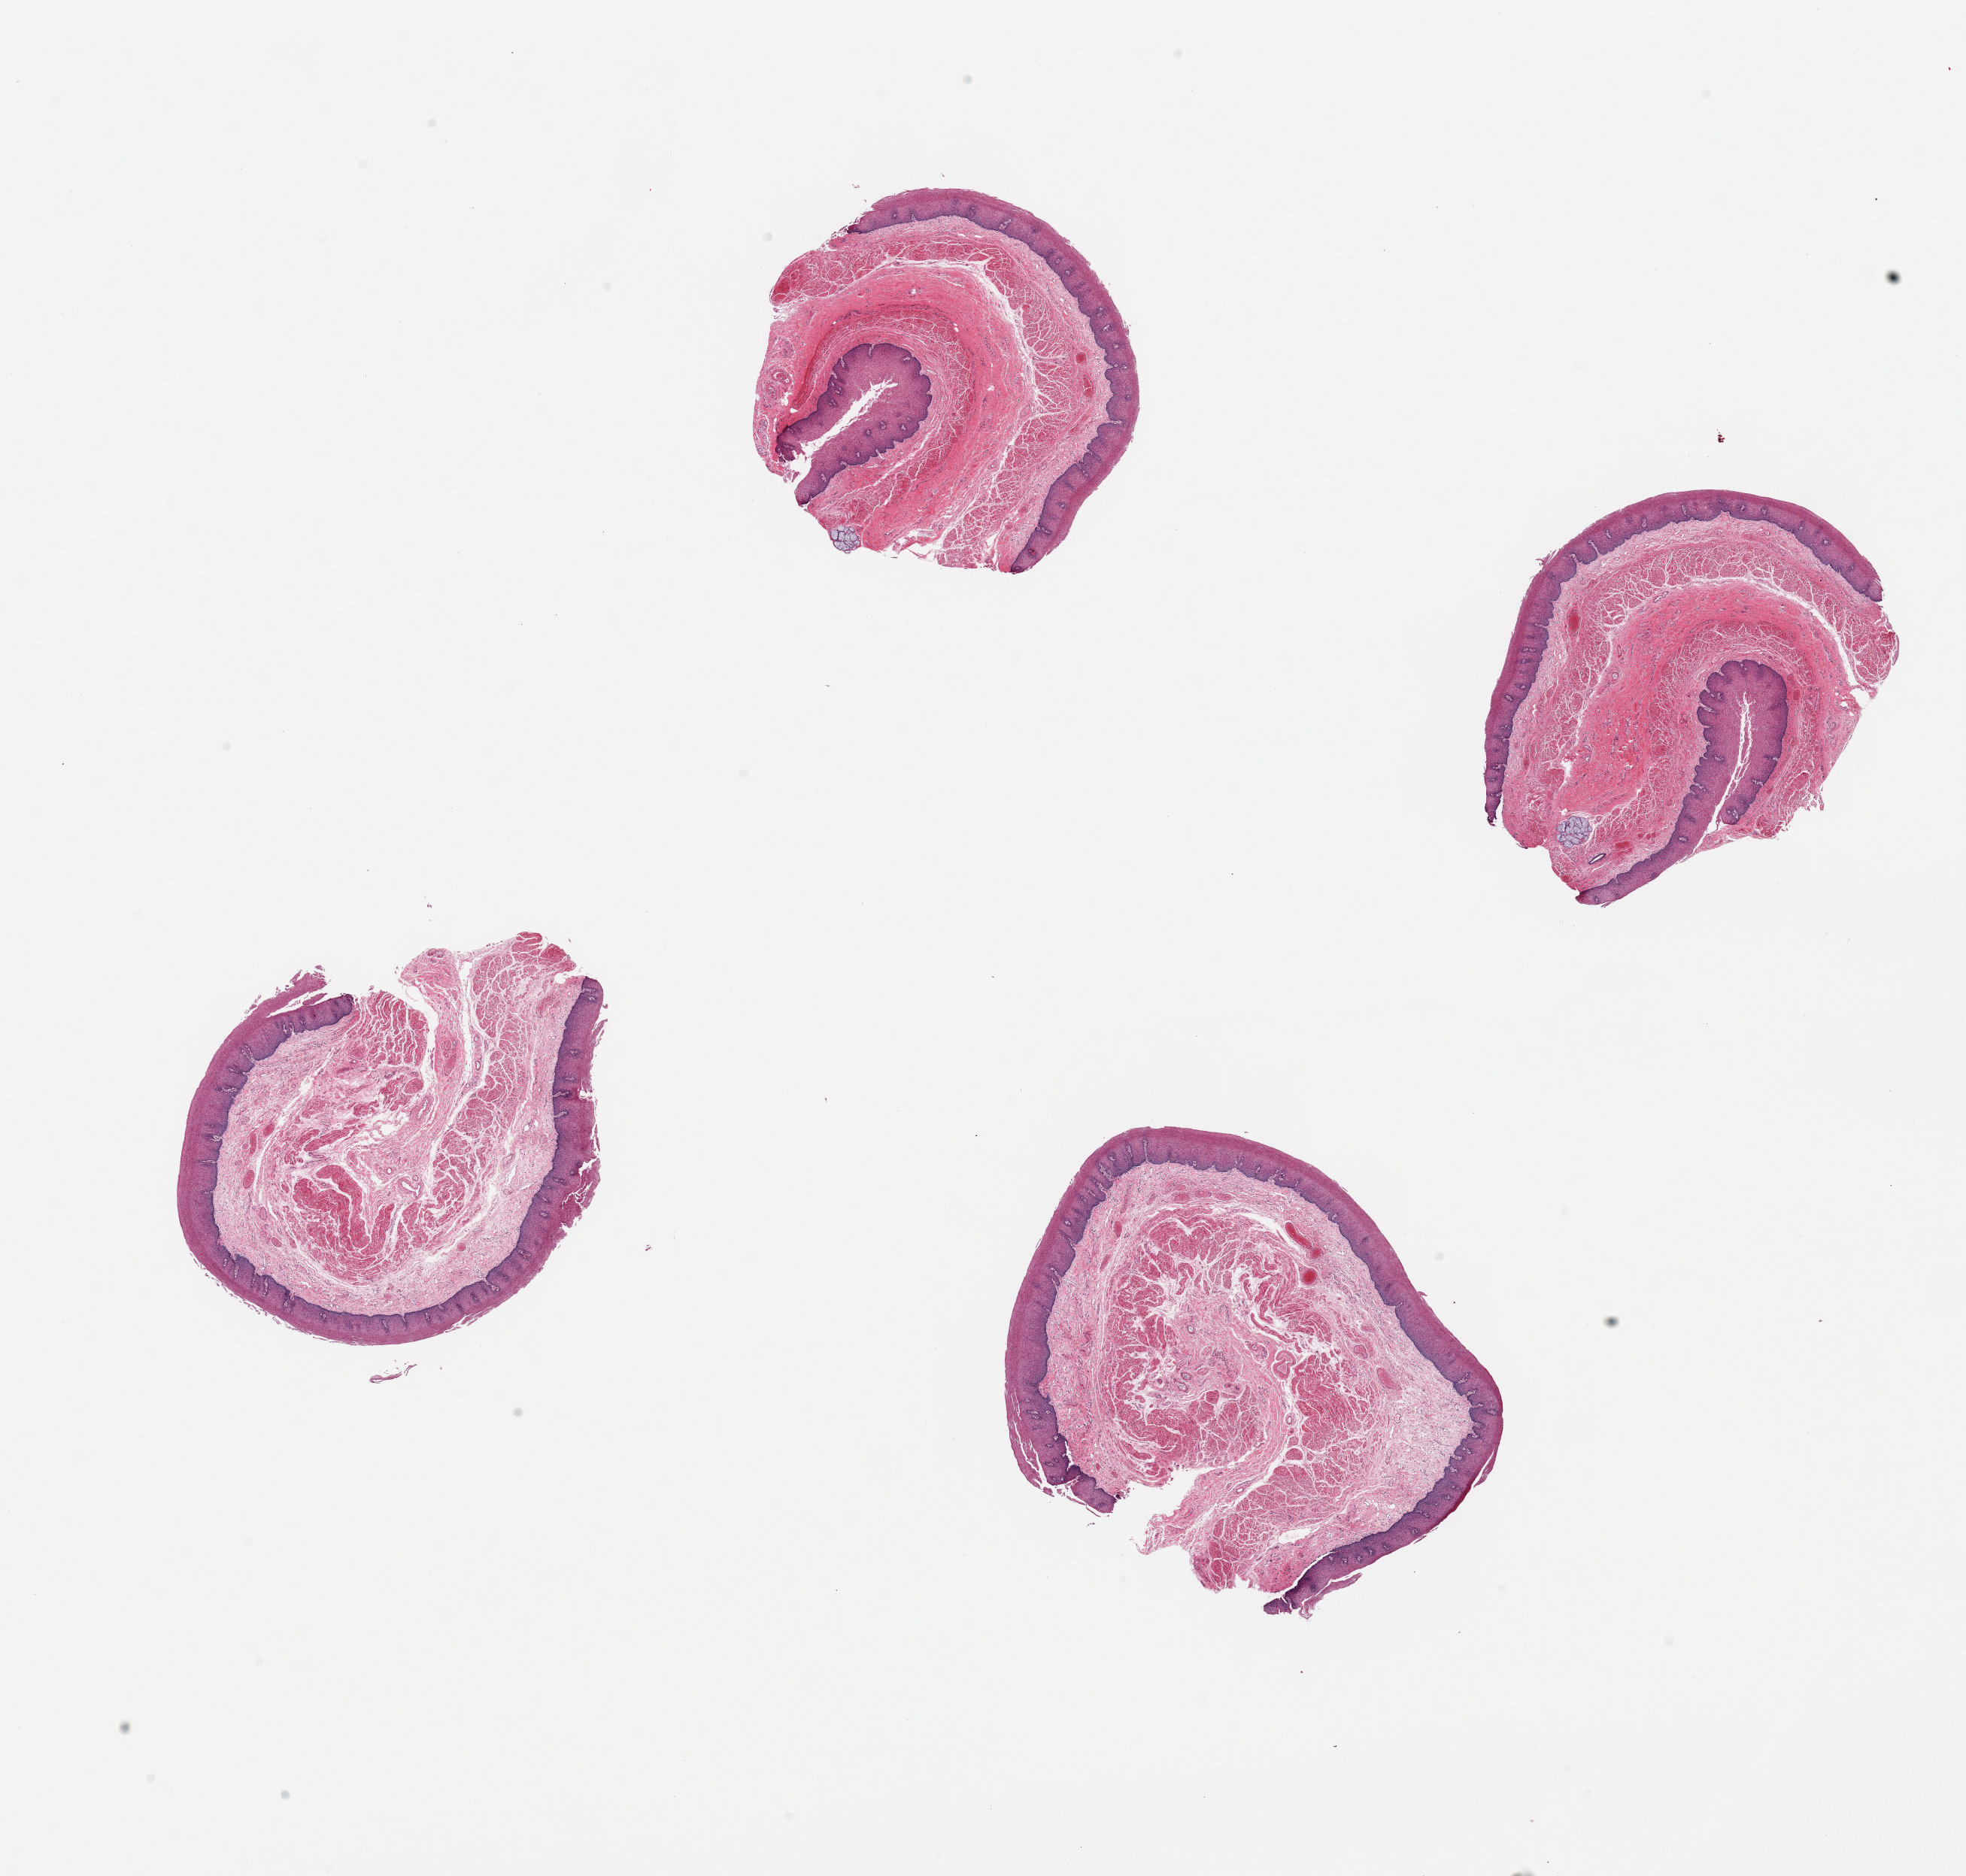
Digitized hematoxylin and eosin (H&E)-stained section — low-resolution overview of the scanned area, about 20.7 x 19.7 mm (from a 20x scan), PAXgene-fixed, paraffin-embedded tissue, section of esophageal mucous membrane (target tissue), tissue donor sample. Donor sex: male.
Pathologist's review note for this sample: 4 pieces, squamous mucosa up to ~0.4mm, 10-20% thickness.